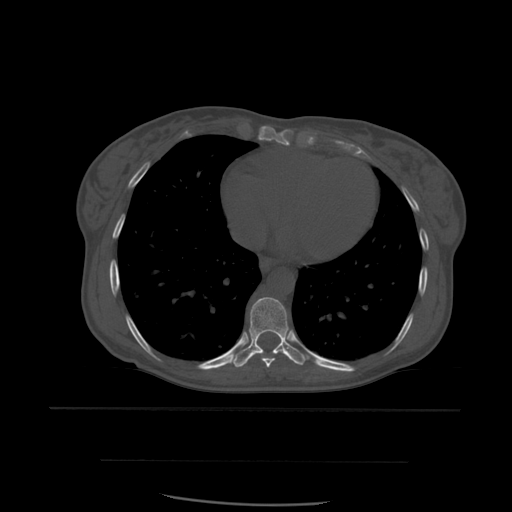
CT including the spine, one axial slice; bone window (W 1800 / L 400 HU); 1.25 mm slice thickness; 512 × 512 image matrix, field of view 392 × 392 mm. Patient age 48 years. Case-level facts recorded for this patient, not image findings: primary cancer: lung.
Annotated regions visible in this slice (semi-automatic segmentation, software-assisted and operator-edited):
- T8 vertebra: bounding box (x1, y1, x2, y2) in pixels: (262, 357, 276, 368)
- T9 vertebra: (233, 297, 309, 368)